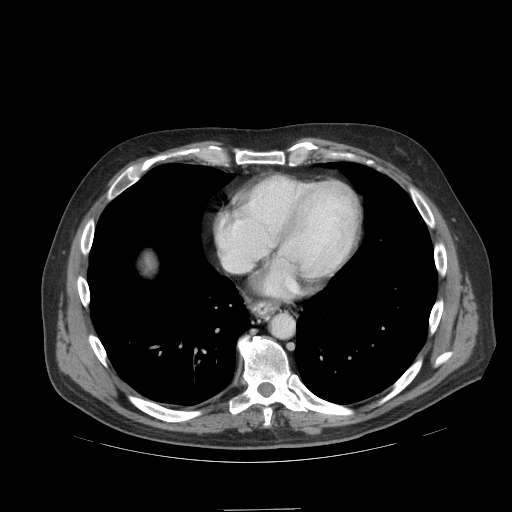
Contrast-enhanced abdominal CT (liver protocol), one axial slice; position 98 of 99 along the scan axis; 140 kVp; soft-tissue window (W 400 / L 40 HU); 2.5 mm slice thickness; 512 × 512 image matrix, field of view 440 × 440 mm. Case-level facts recorded for this patient, not image findings: diagnosis: hepatocellular carcinoma (patient treated with transarterial chemoembolisation; whether this scan precedes or follows treatment is not stated here); TNM stage (as recorded): Stage-I; Child-Pugh class: A.
Outlined on this slice (semi-automatically segmented with operator editing):
- abdominal aorta: bounding box [x1, y1, x2, y2] px = [273, 315, 293, 337]
- liver parenchyma outside the tumour (the mass and vessels are separate outlines, so this box may not span the whole liver): [144, 254, 154, 271]